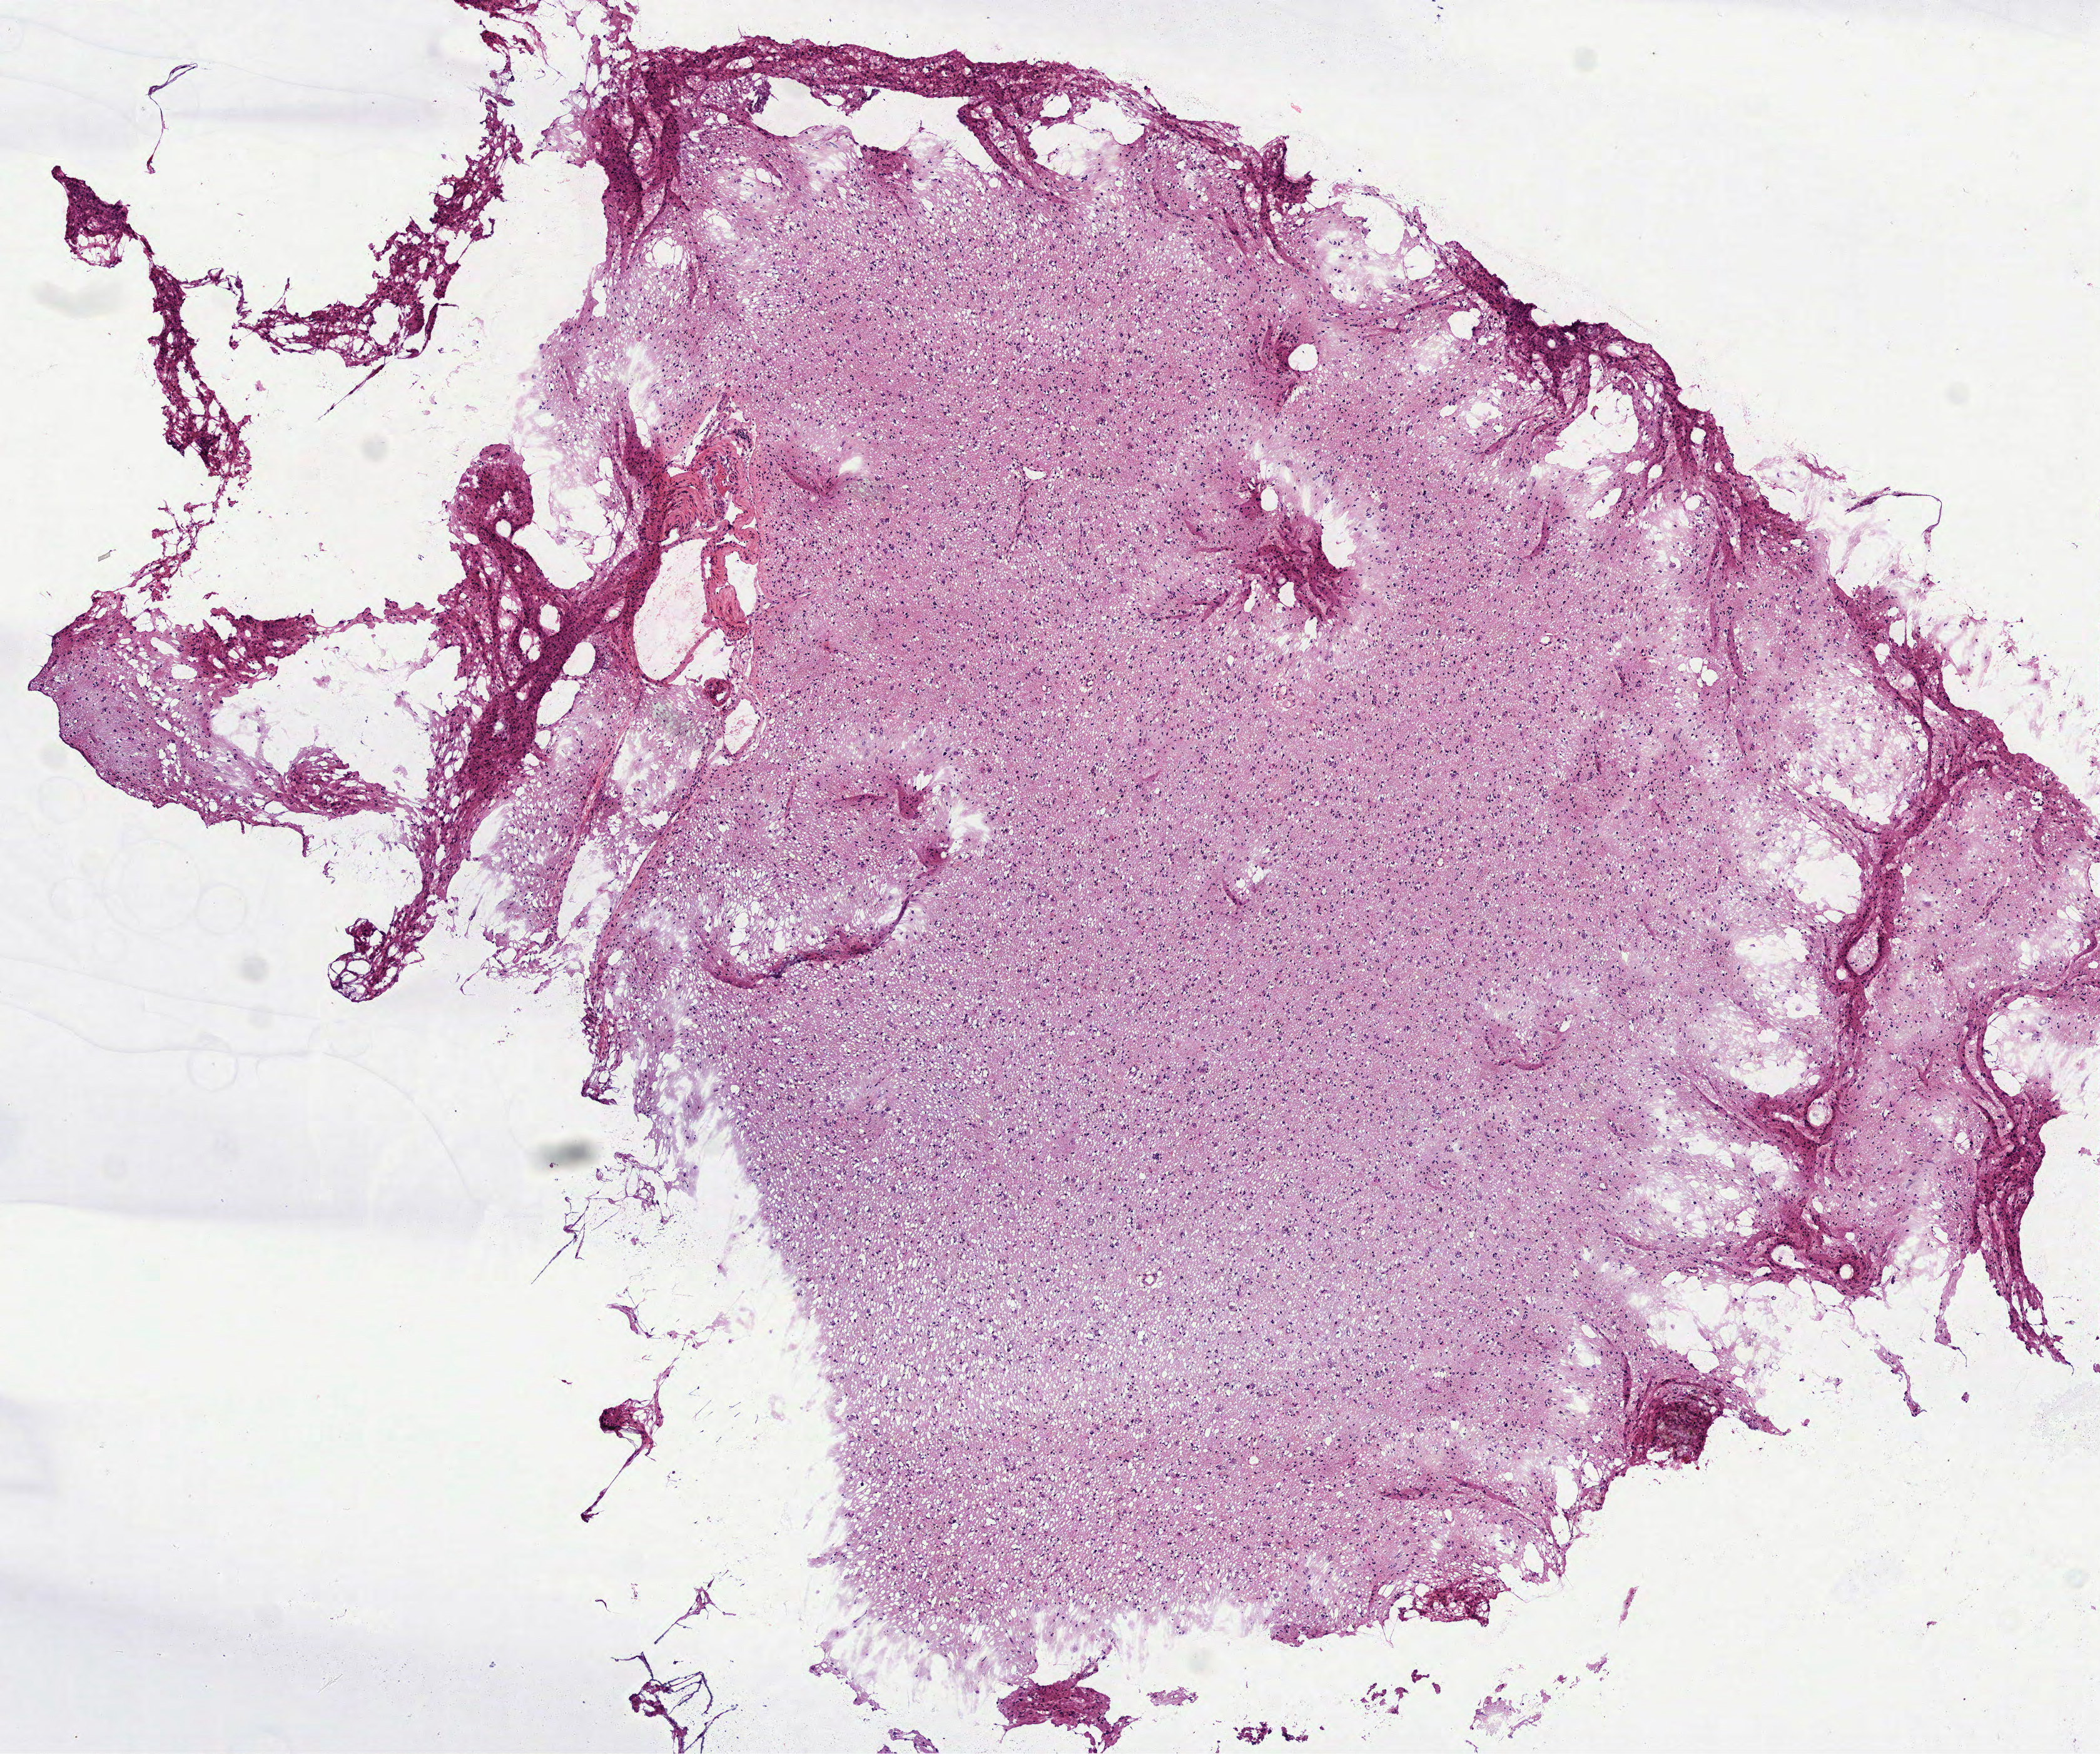
Whole-slide histology image, H&E-stained — shown as a low-resolution overview of the whole scanned area (about 6.8 x 5.7 mm). Frozen section from the top of the tissue portion. Sample: primary tumour, brain. Patient: male, age at initial diagnosis 37 years. Histologic grade: G3 (poorly differentiated). Pathologist review of this section (percent, as recorded): tumour cells 100%, tumour nuclei 70%, normal cells 0%, stromal cells 0%, necrosis 0%.
Laterality: right. Histologic diagnosis: Oligodendroglioma, anaplastic.